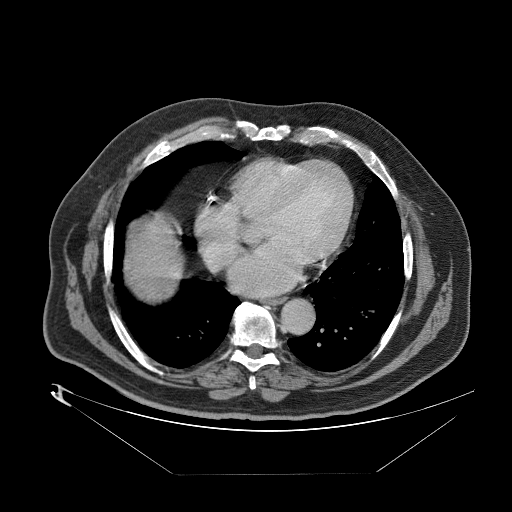
Contrast-enhanced abdominal CT (liver protocol), one axial slice. 140 kVp. One of 2 acquisitions stored at this slice position. Soft-tissue window (W 400 / L 40 HU). 2.5 mm slice thickness. 512 × 512 image matrix. From the clinical record (not read from this slice): diagnosis: hepatocellular carcinoma (patient treated with transarterial chemoembolisation; whether this scan precedes or follows treatment is not stated here); TNM stage (as recorded): Stage-II; Child-Pugh class: B; tumour differentiation: moderately differentiated; tumour nodularity: multinodular.
Outlined on this slice (semi-automatically segmented with operator editing):
- abdominal aorta: box from (x=279, y=298) to (x=313, y=333) px
- liver parenchyma outside the tumour (the mass and vessels are separate outlines, so this box may not span the whole liver): (x=136, y=232)–(x=160, y=261)